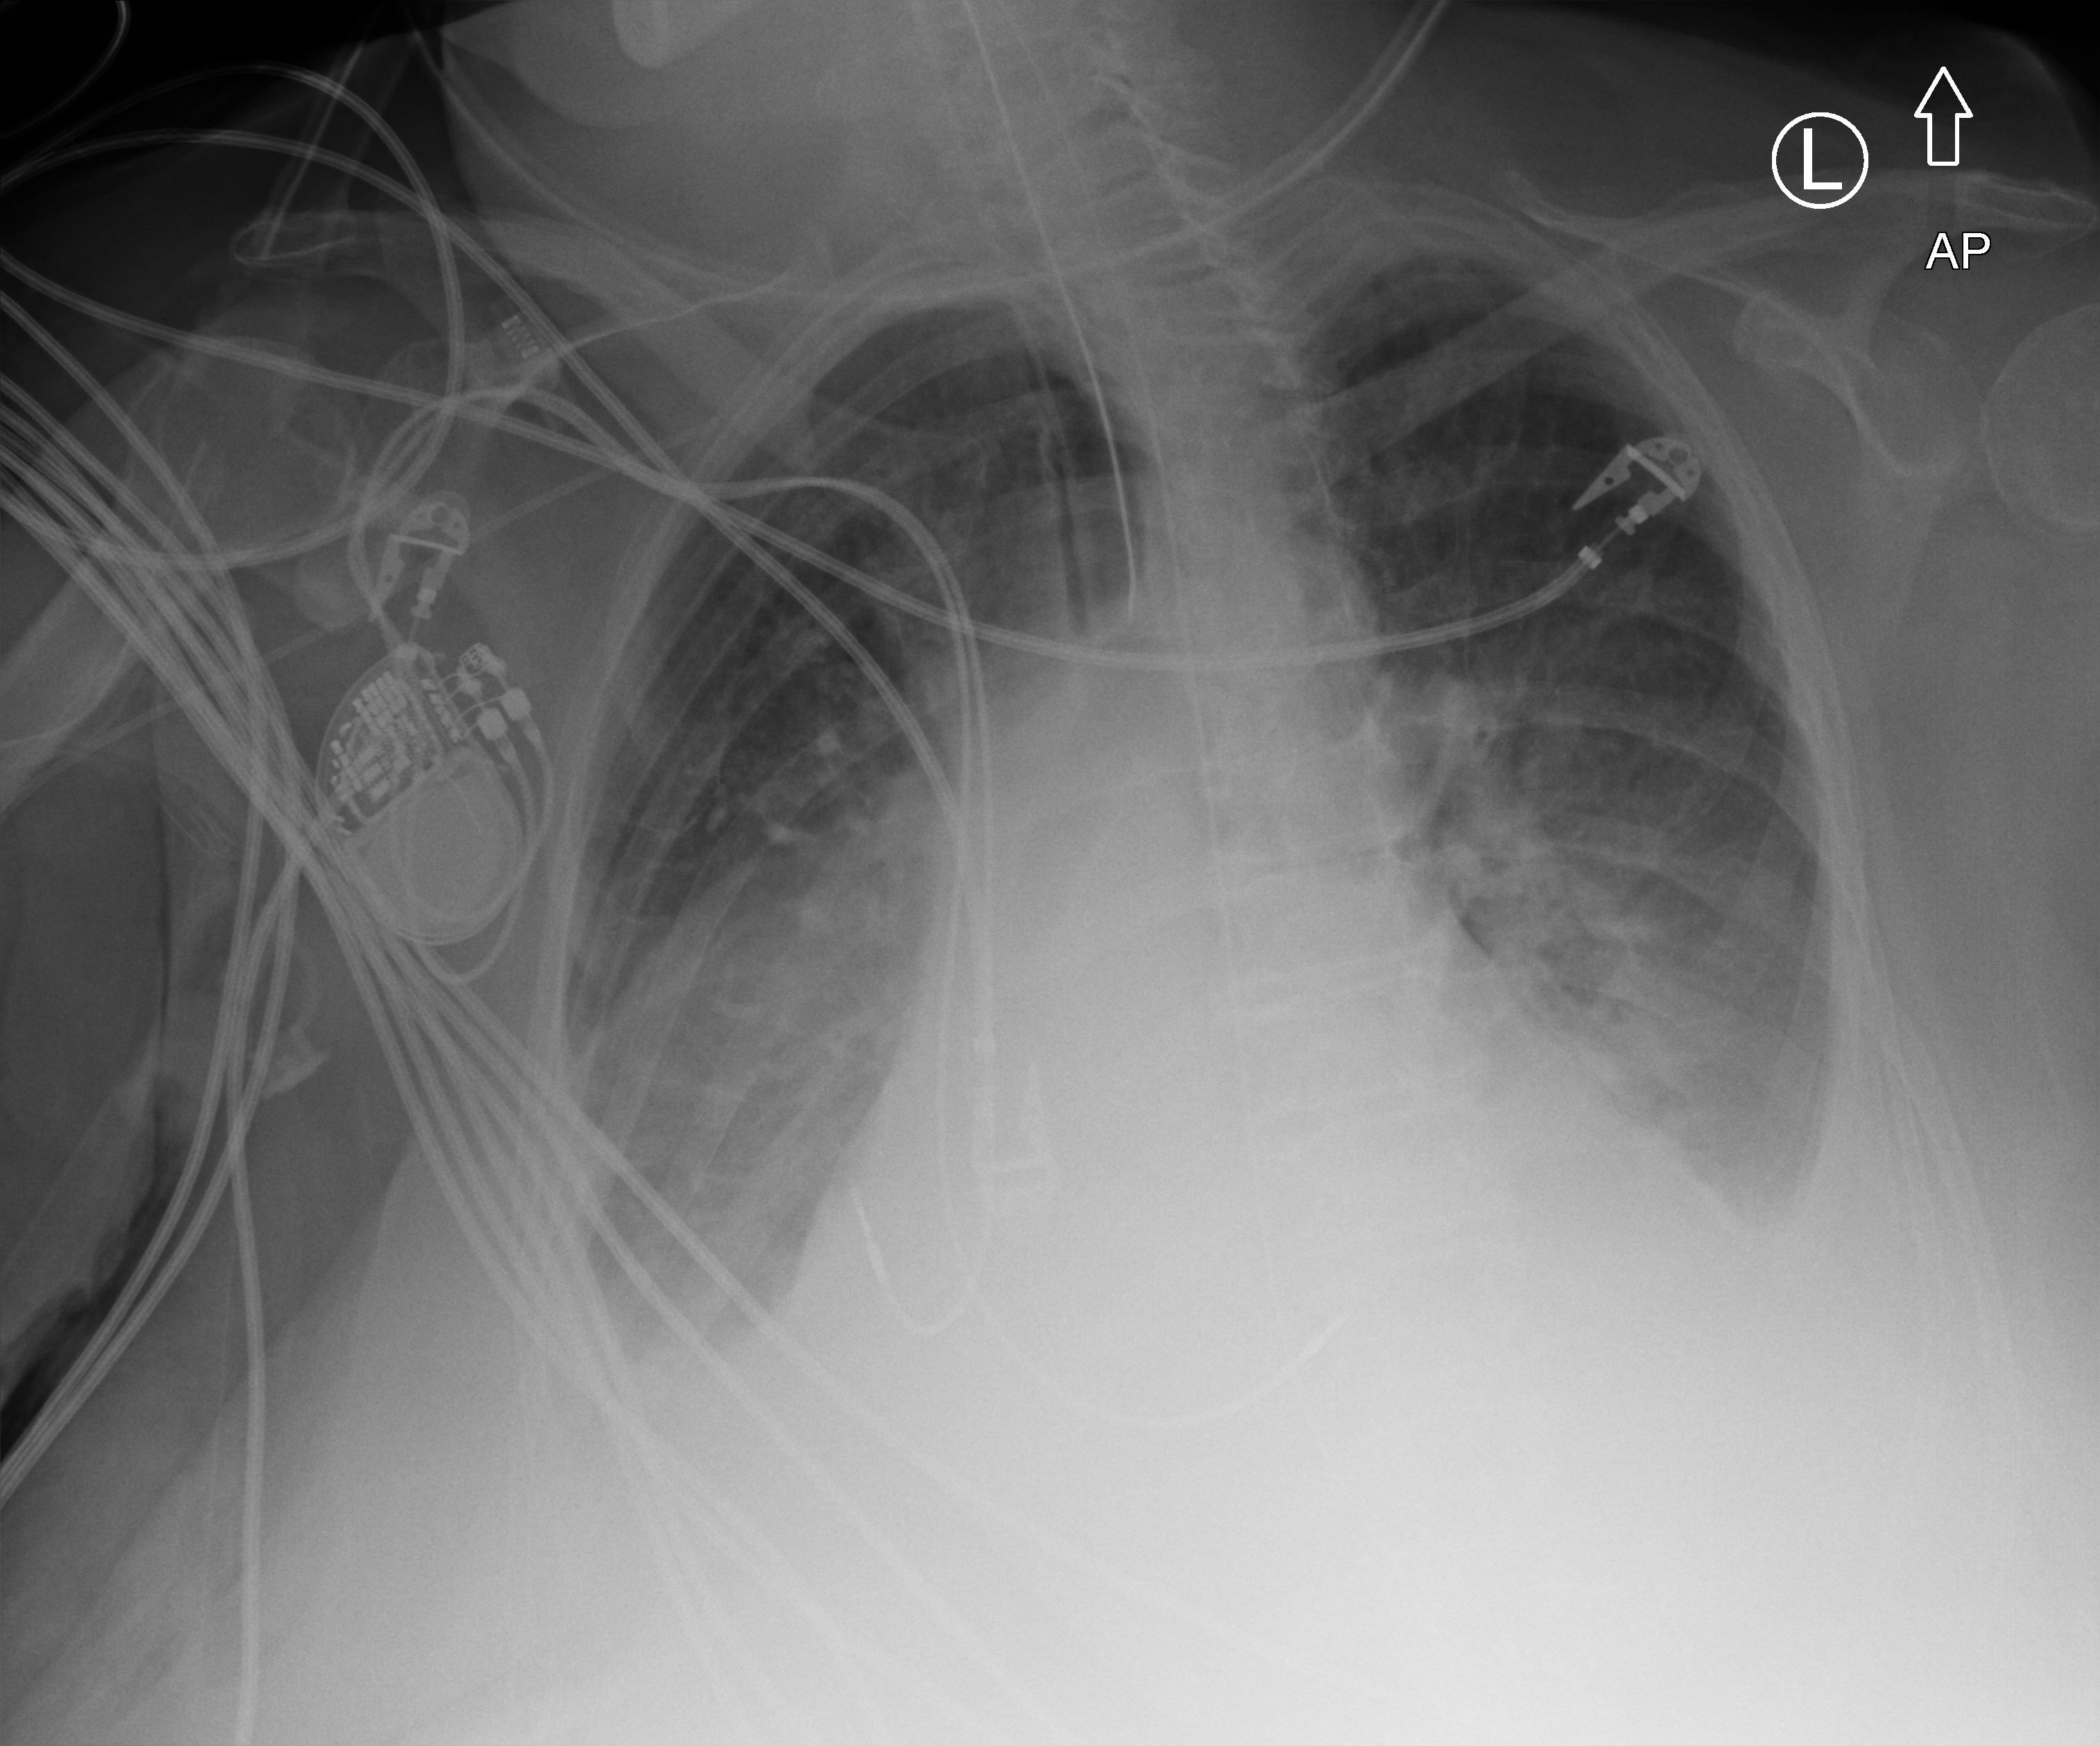
Chest X-ray (portable); anteroposterior (AP) projection. Patient hospitalised with COVID-19; female, aged 75–90 years.
Admission-level facts for this patient (not findings on this image; timing relative to this image not recorded): length of hospital stay: 21 days; mechanically ventilated during this hospital stay: yes.